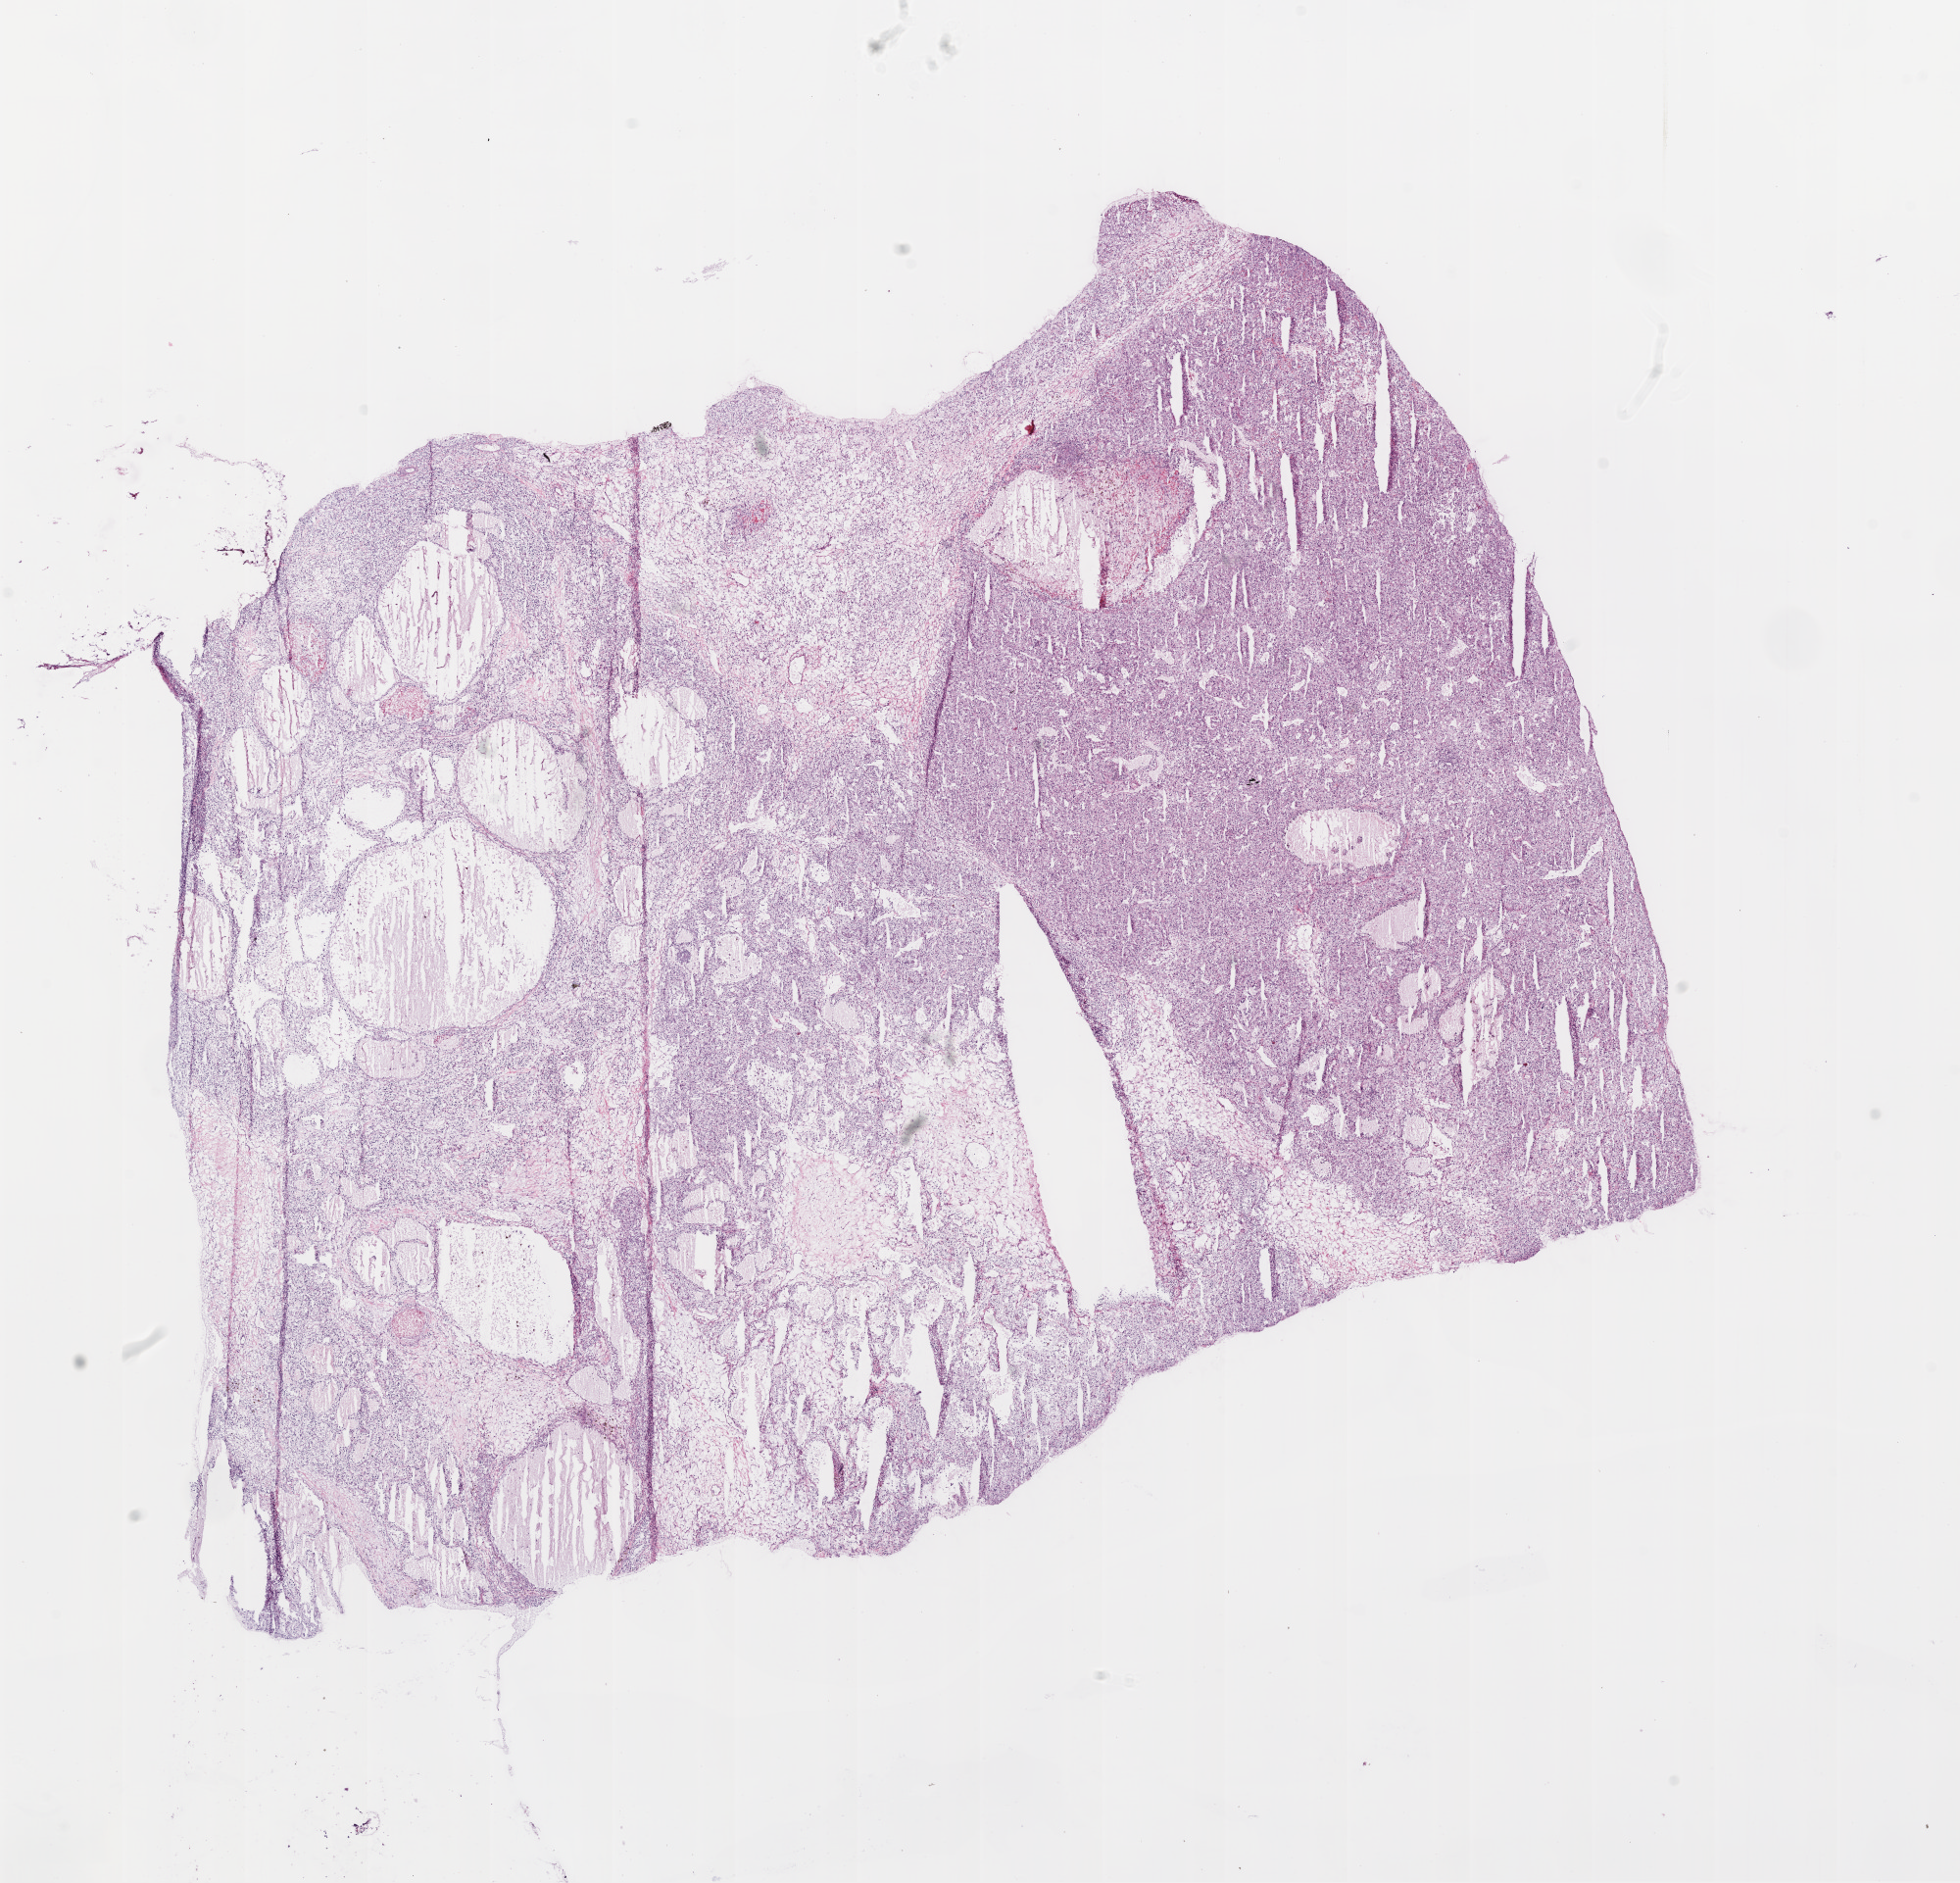
Whole-slide histology image, H&E-stained — low-resolution overview of the scanned area, about 16.0 x 15.4 mm. Frozen section from the bottom of the tissue portion. Kidney, primary tumour sample. Male patient; age at initial diagnosis 52 years. Histologic grade: G2 (moderately differentiated). Slide review estimates, as recorded: tumour cells 90%, tumour nuclei 90%, normal cells 0%, stromal cells 10%, necrosis 0%.
AJCC pathologic stage: I. Histologic diagnosis: Clear cell adenocarcinoma, NOS.